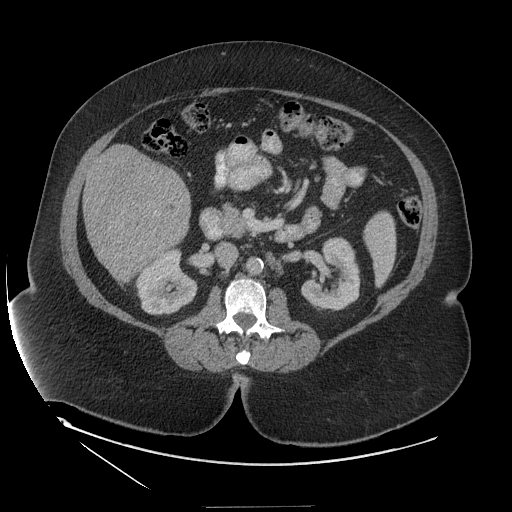
Contrast-enhanced abdominal CT (liver protocol), one axial slice. Slice 49 of 127 in the series (ordered by position). 140 kVp. Soft-tissue window (W 400 / L 40 HU). 512 × 512 image matrix, field of view 480 × 480 mm. Case-level facts recorded for this patient, not image findings: diagnosis: hepatocellular carcinoma (patient treated with transarterial chemoembolisation; whether this scan precedes or follows treatment is not stated here); TNM stage (as recorded): Stage-II; Child-Pugh class: A.
Structures marked on this image (semi-automatically segmented with operator editing):
- liver parenchyma outside the tumour (the mass and vessels are separate outlines, so this box may not span the whole liver): bounding box <82,144,190,282> (left, top, right, bottom; pixels)